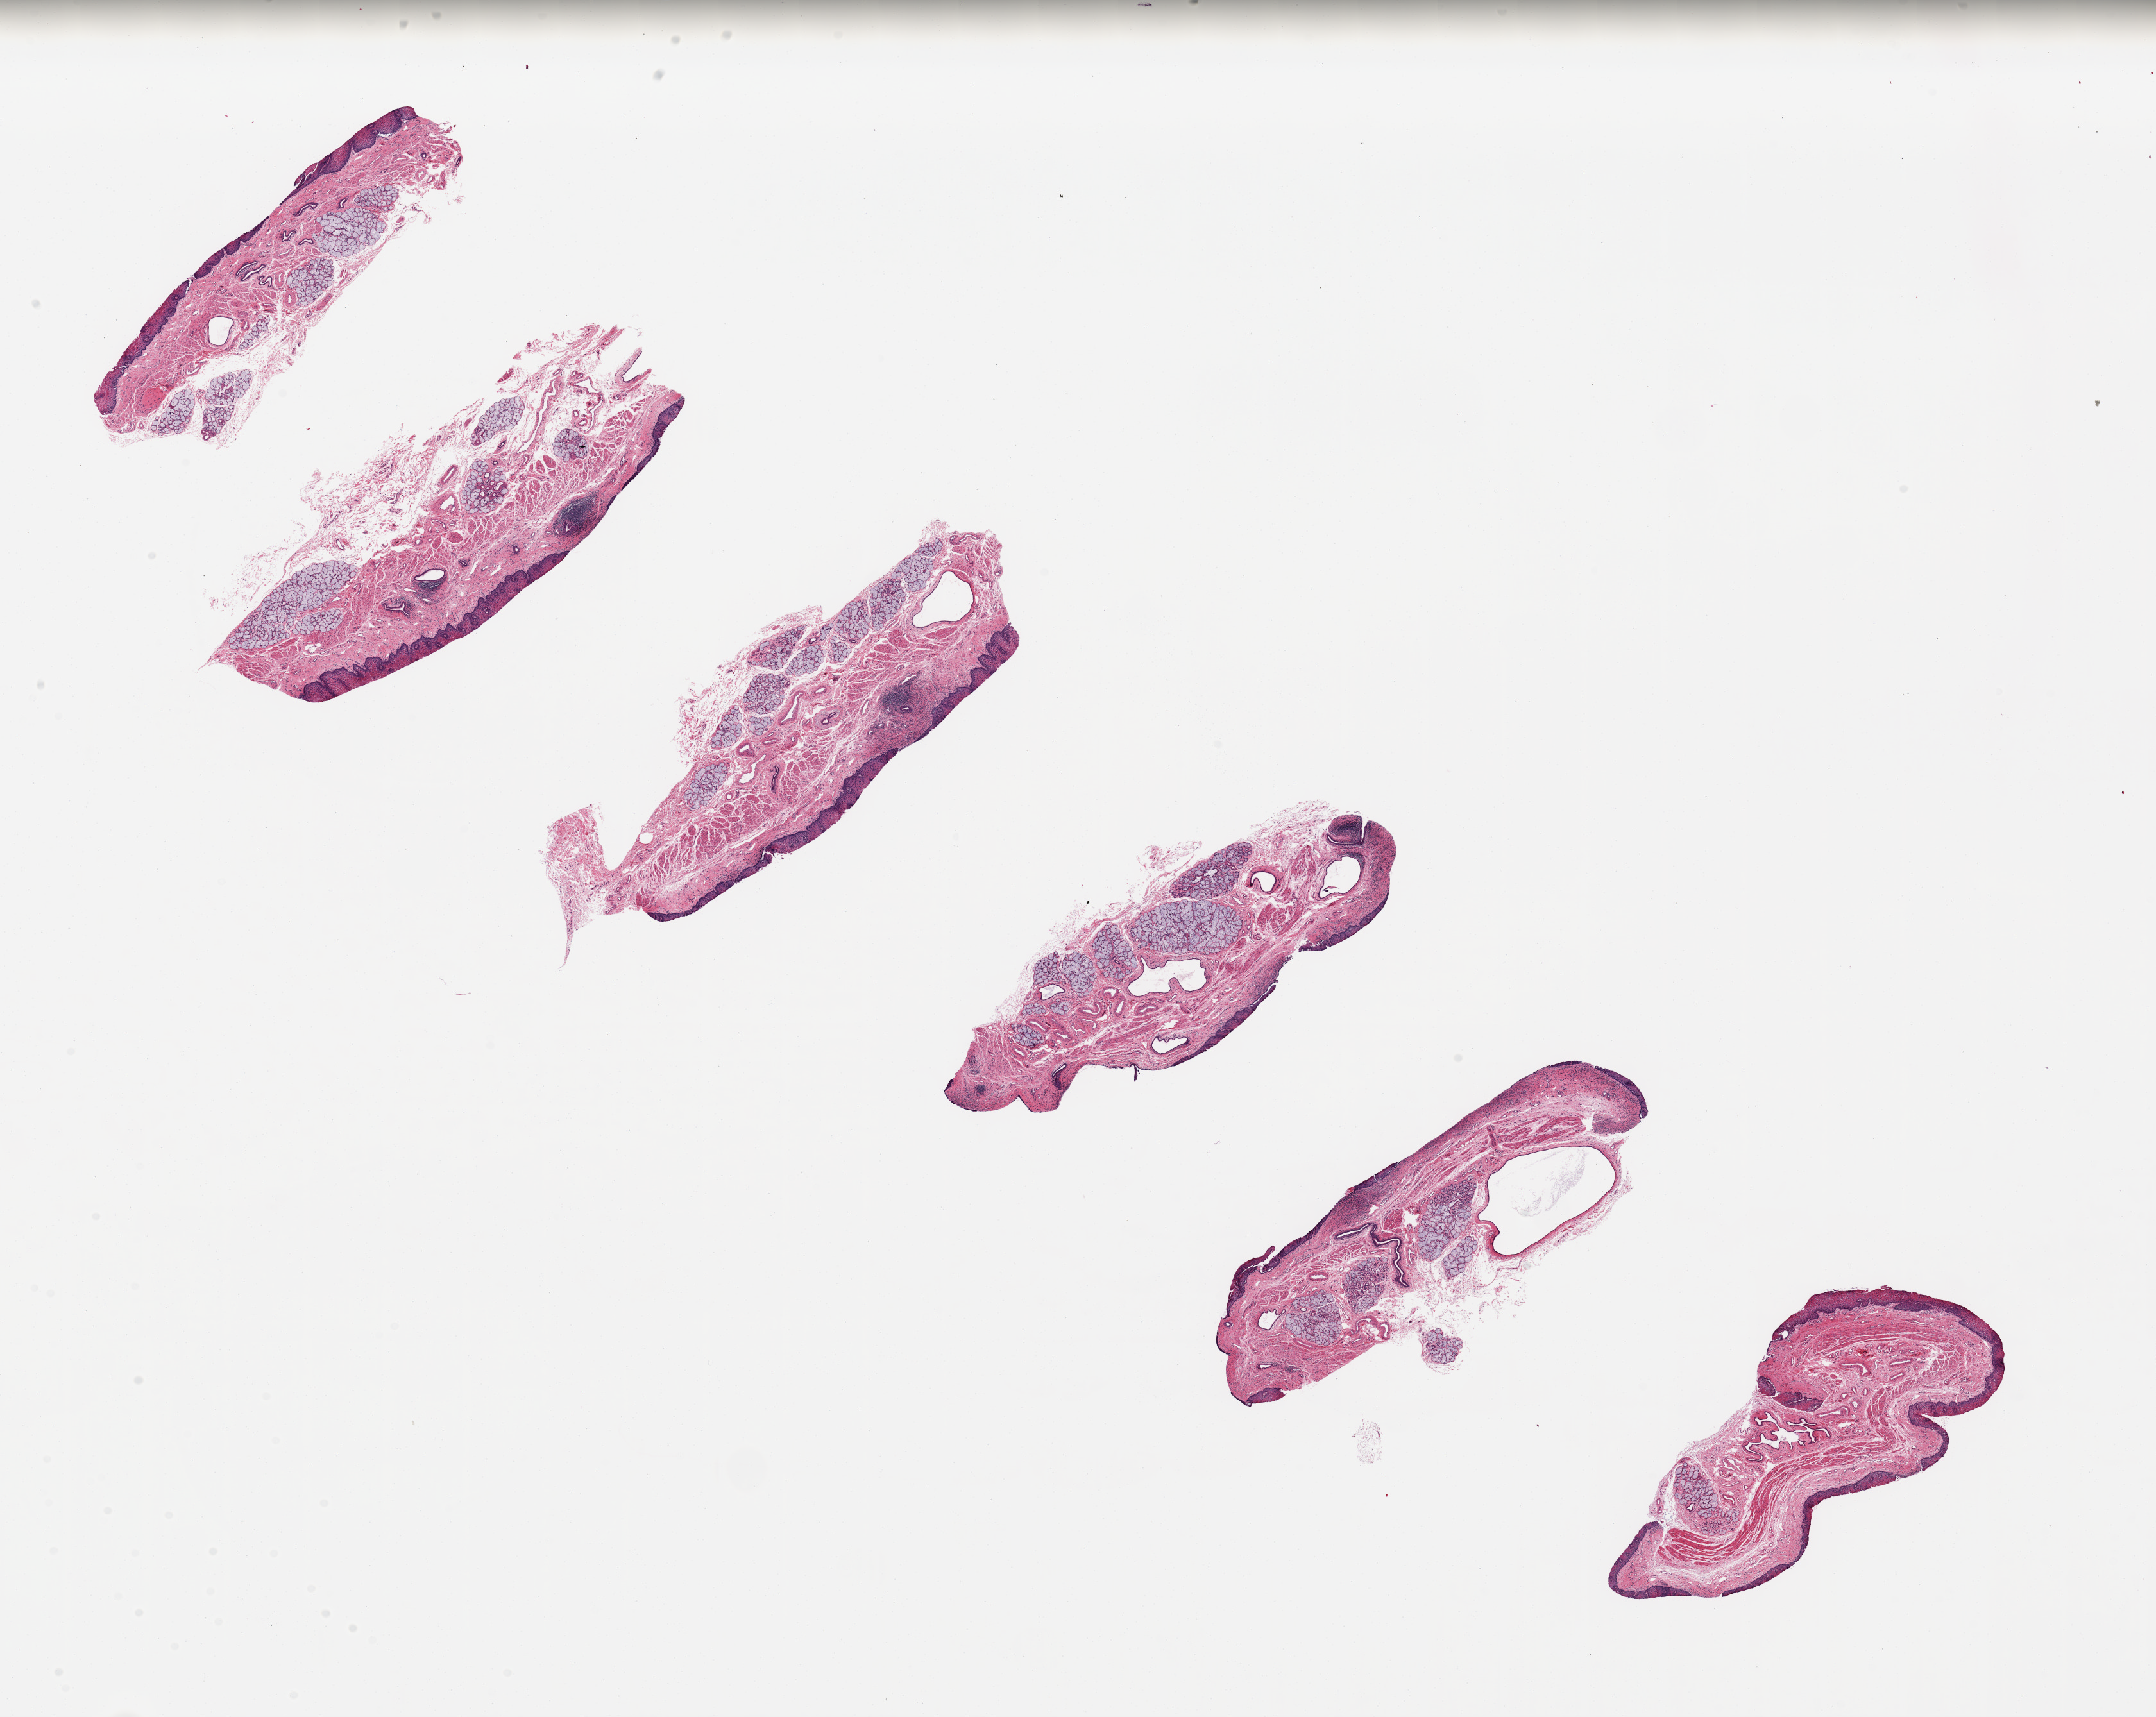
Haematoxylin and eosin whole-slide image, whole scanned area (about 26.6 x 21.2 mm, acquisition: 20x scan) shown as a low-resolution overview; PAXgene-fixed, paraffin-embedded tissue; section of esophageal mucous membrane (target tissue); donor tissue sample. Male donor.
Reviewer comment on this tissue sample: 6 ~6x2mm pieces. Squamous mucosa is ~10% of thickness. Patchy focally intense chronic esophagitis.